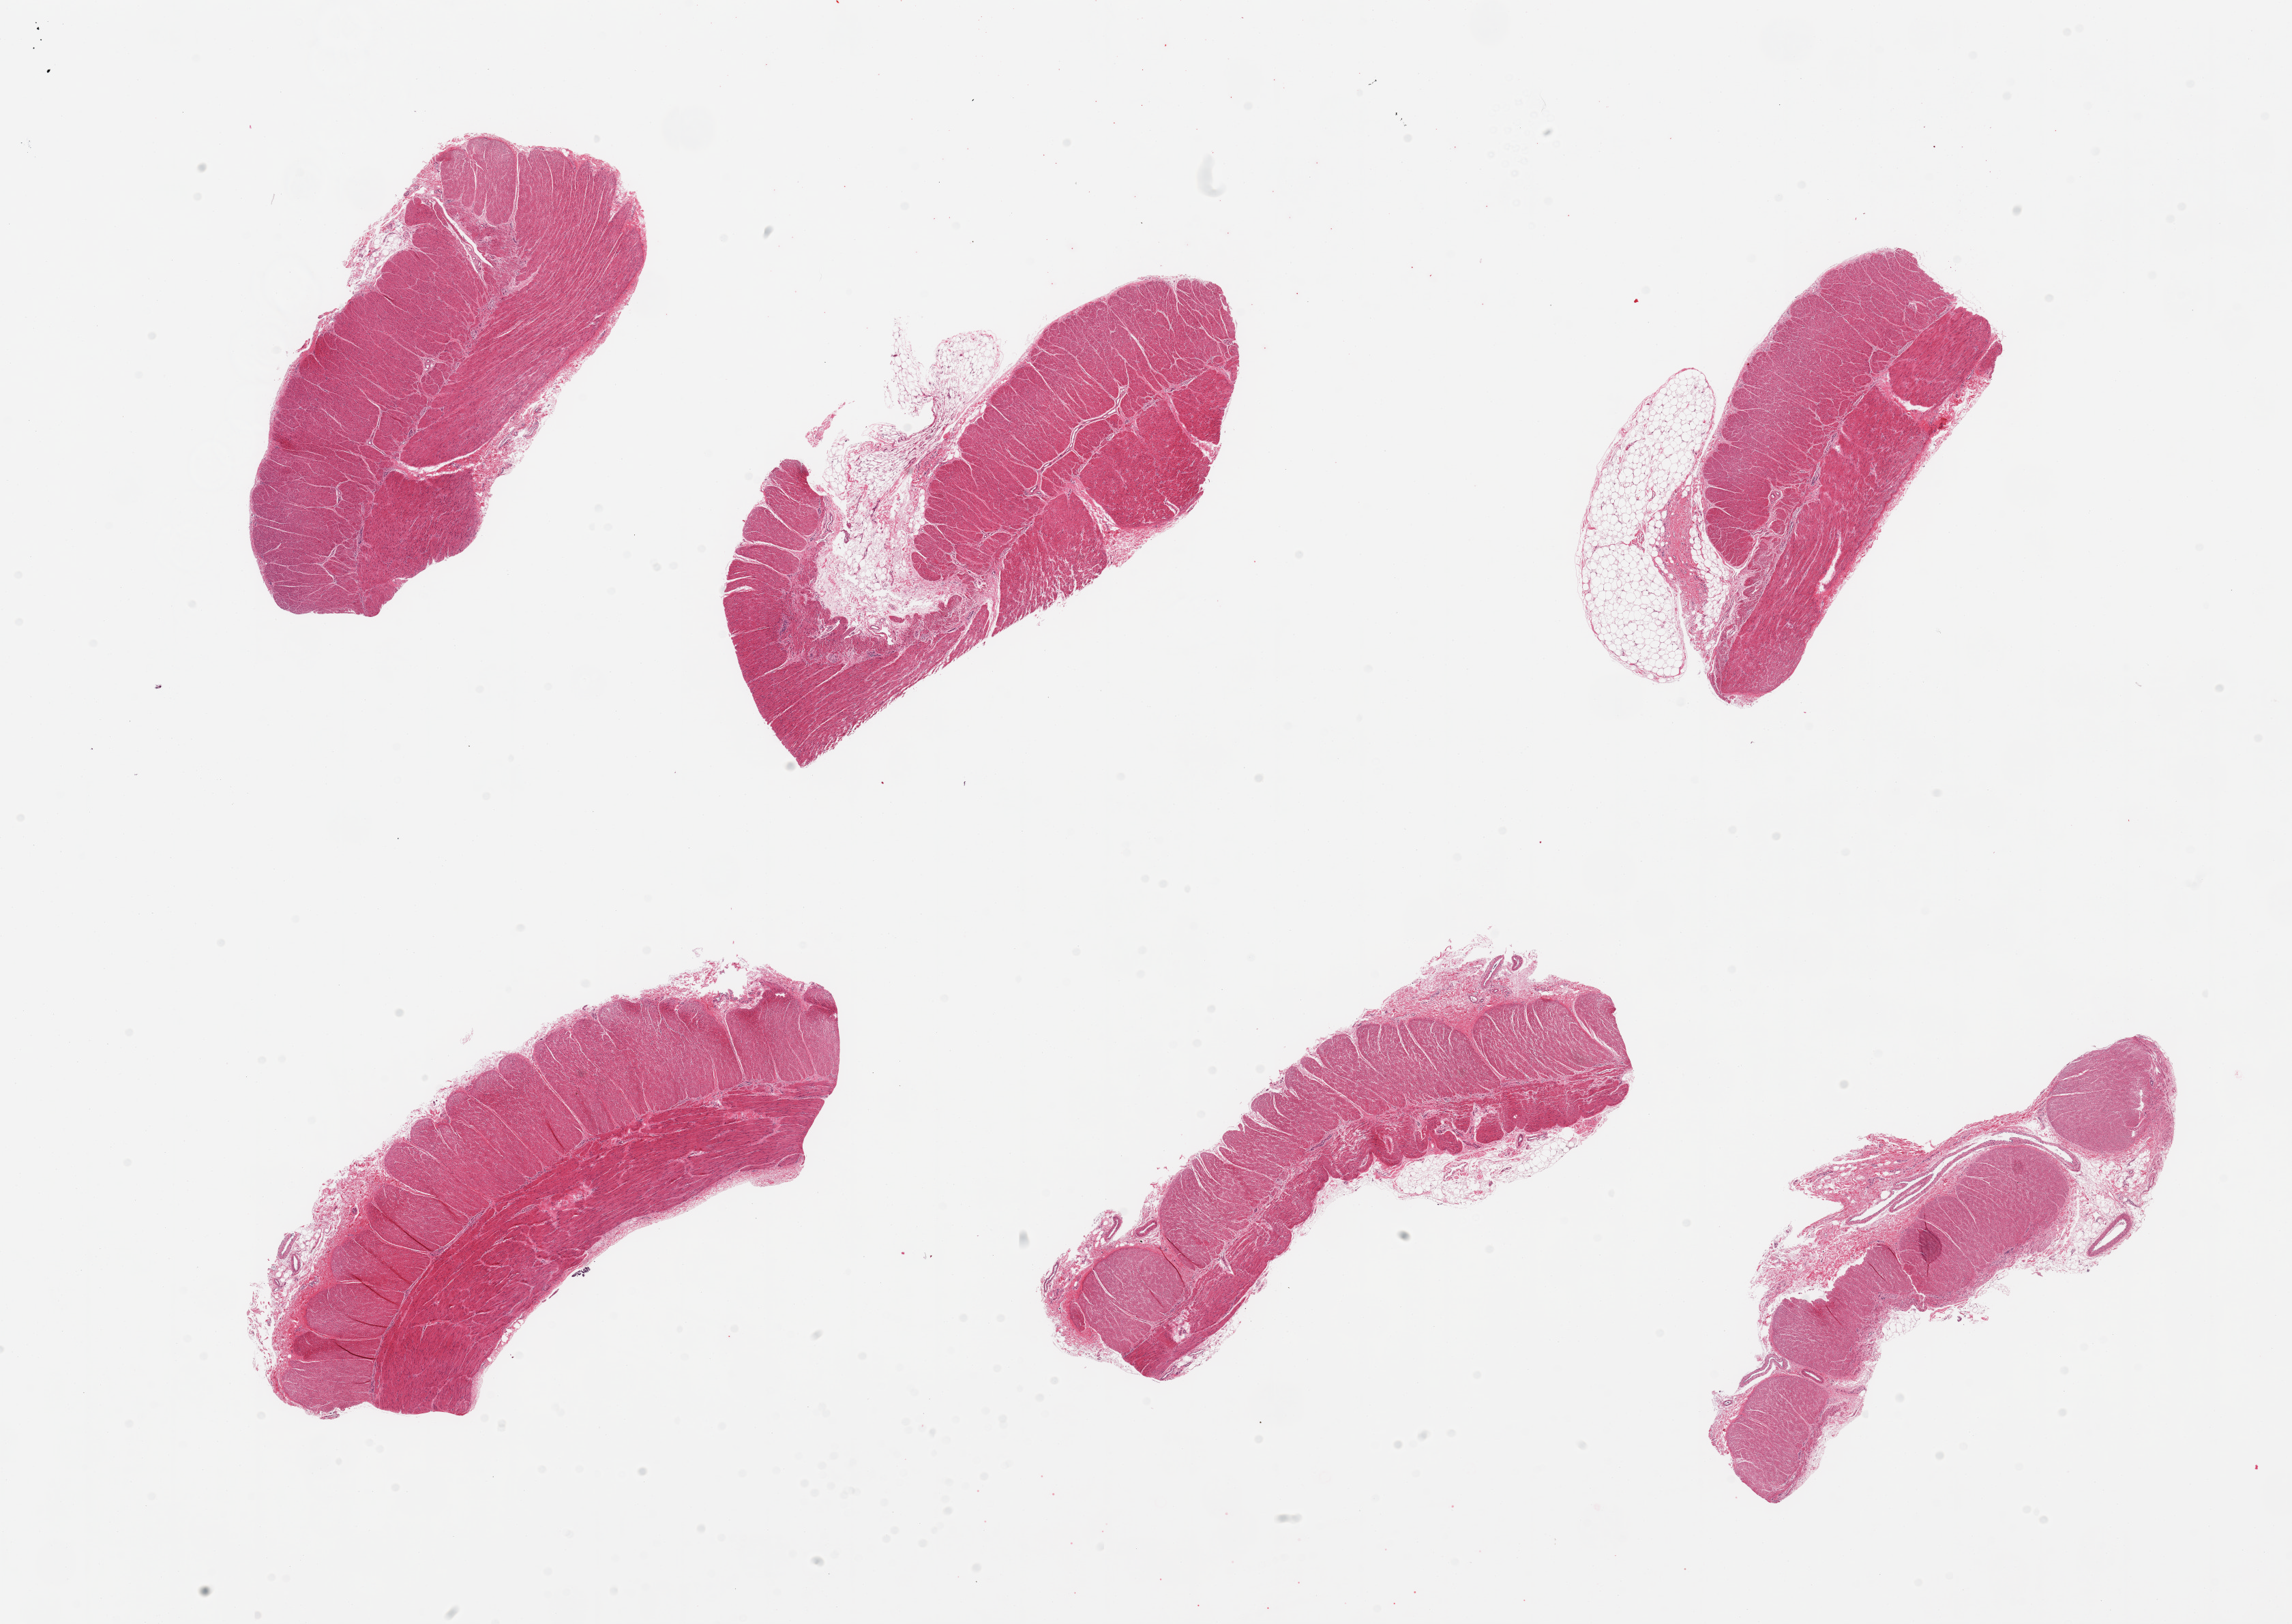
H&E whole-slide image, whole scanned area (about 26.6 x 18.8 mm) shown as a low-resolution overview. PAXgene-fixed paraffin-embedded (PFPE) section. Sampled site (target tissue): sigmoid colon. Tissue donor sample. Donor sex: female.
Pathologist's review note for this sample: 6 pieces; varying amounts of submucosal fat.